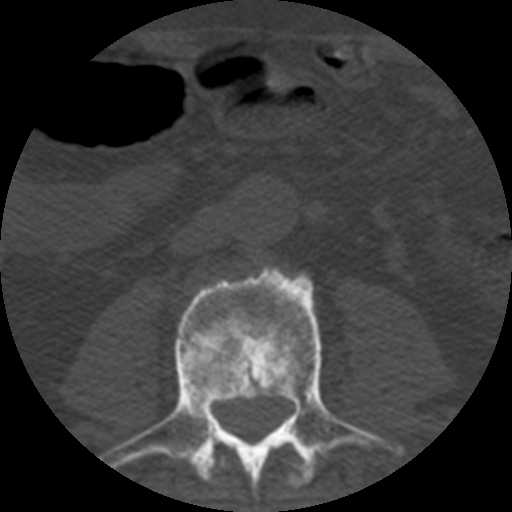
CT including the spine, one axial slice. Reconstruction kernel STANDARD. 120 kVp. Bone window (W 1800 / L 400 HU). 512 × 512 image matrix, field of view 160 × 160 mm. Patient age 57 years. From the clinical record (not read from this slice): primary cancer: prostate.
Structures marked on this image (semi-automatically segmented with operator editing):
- L2 vertebra: box from (x=213, y=441) to (x=314, y=488) px
- L3 vertebra: (x=102, y=267)–(x=404, y=491)